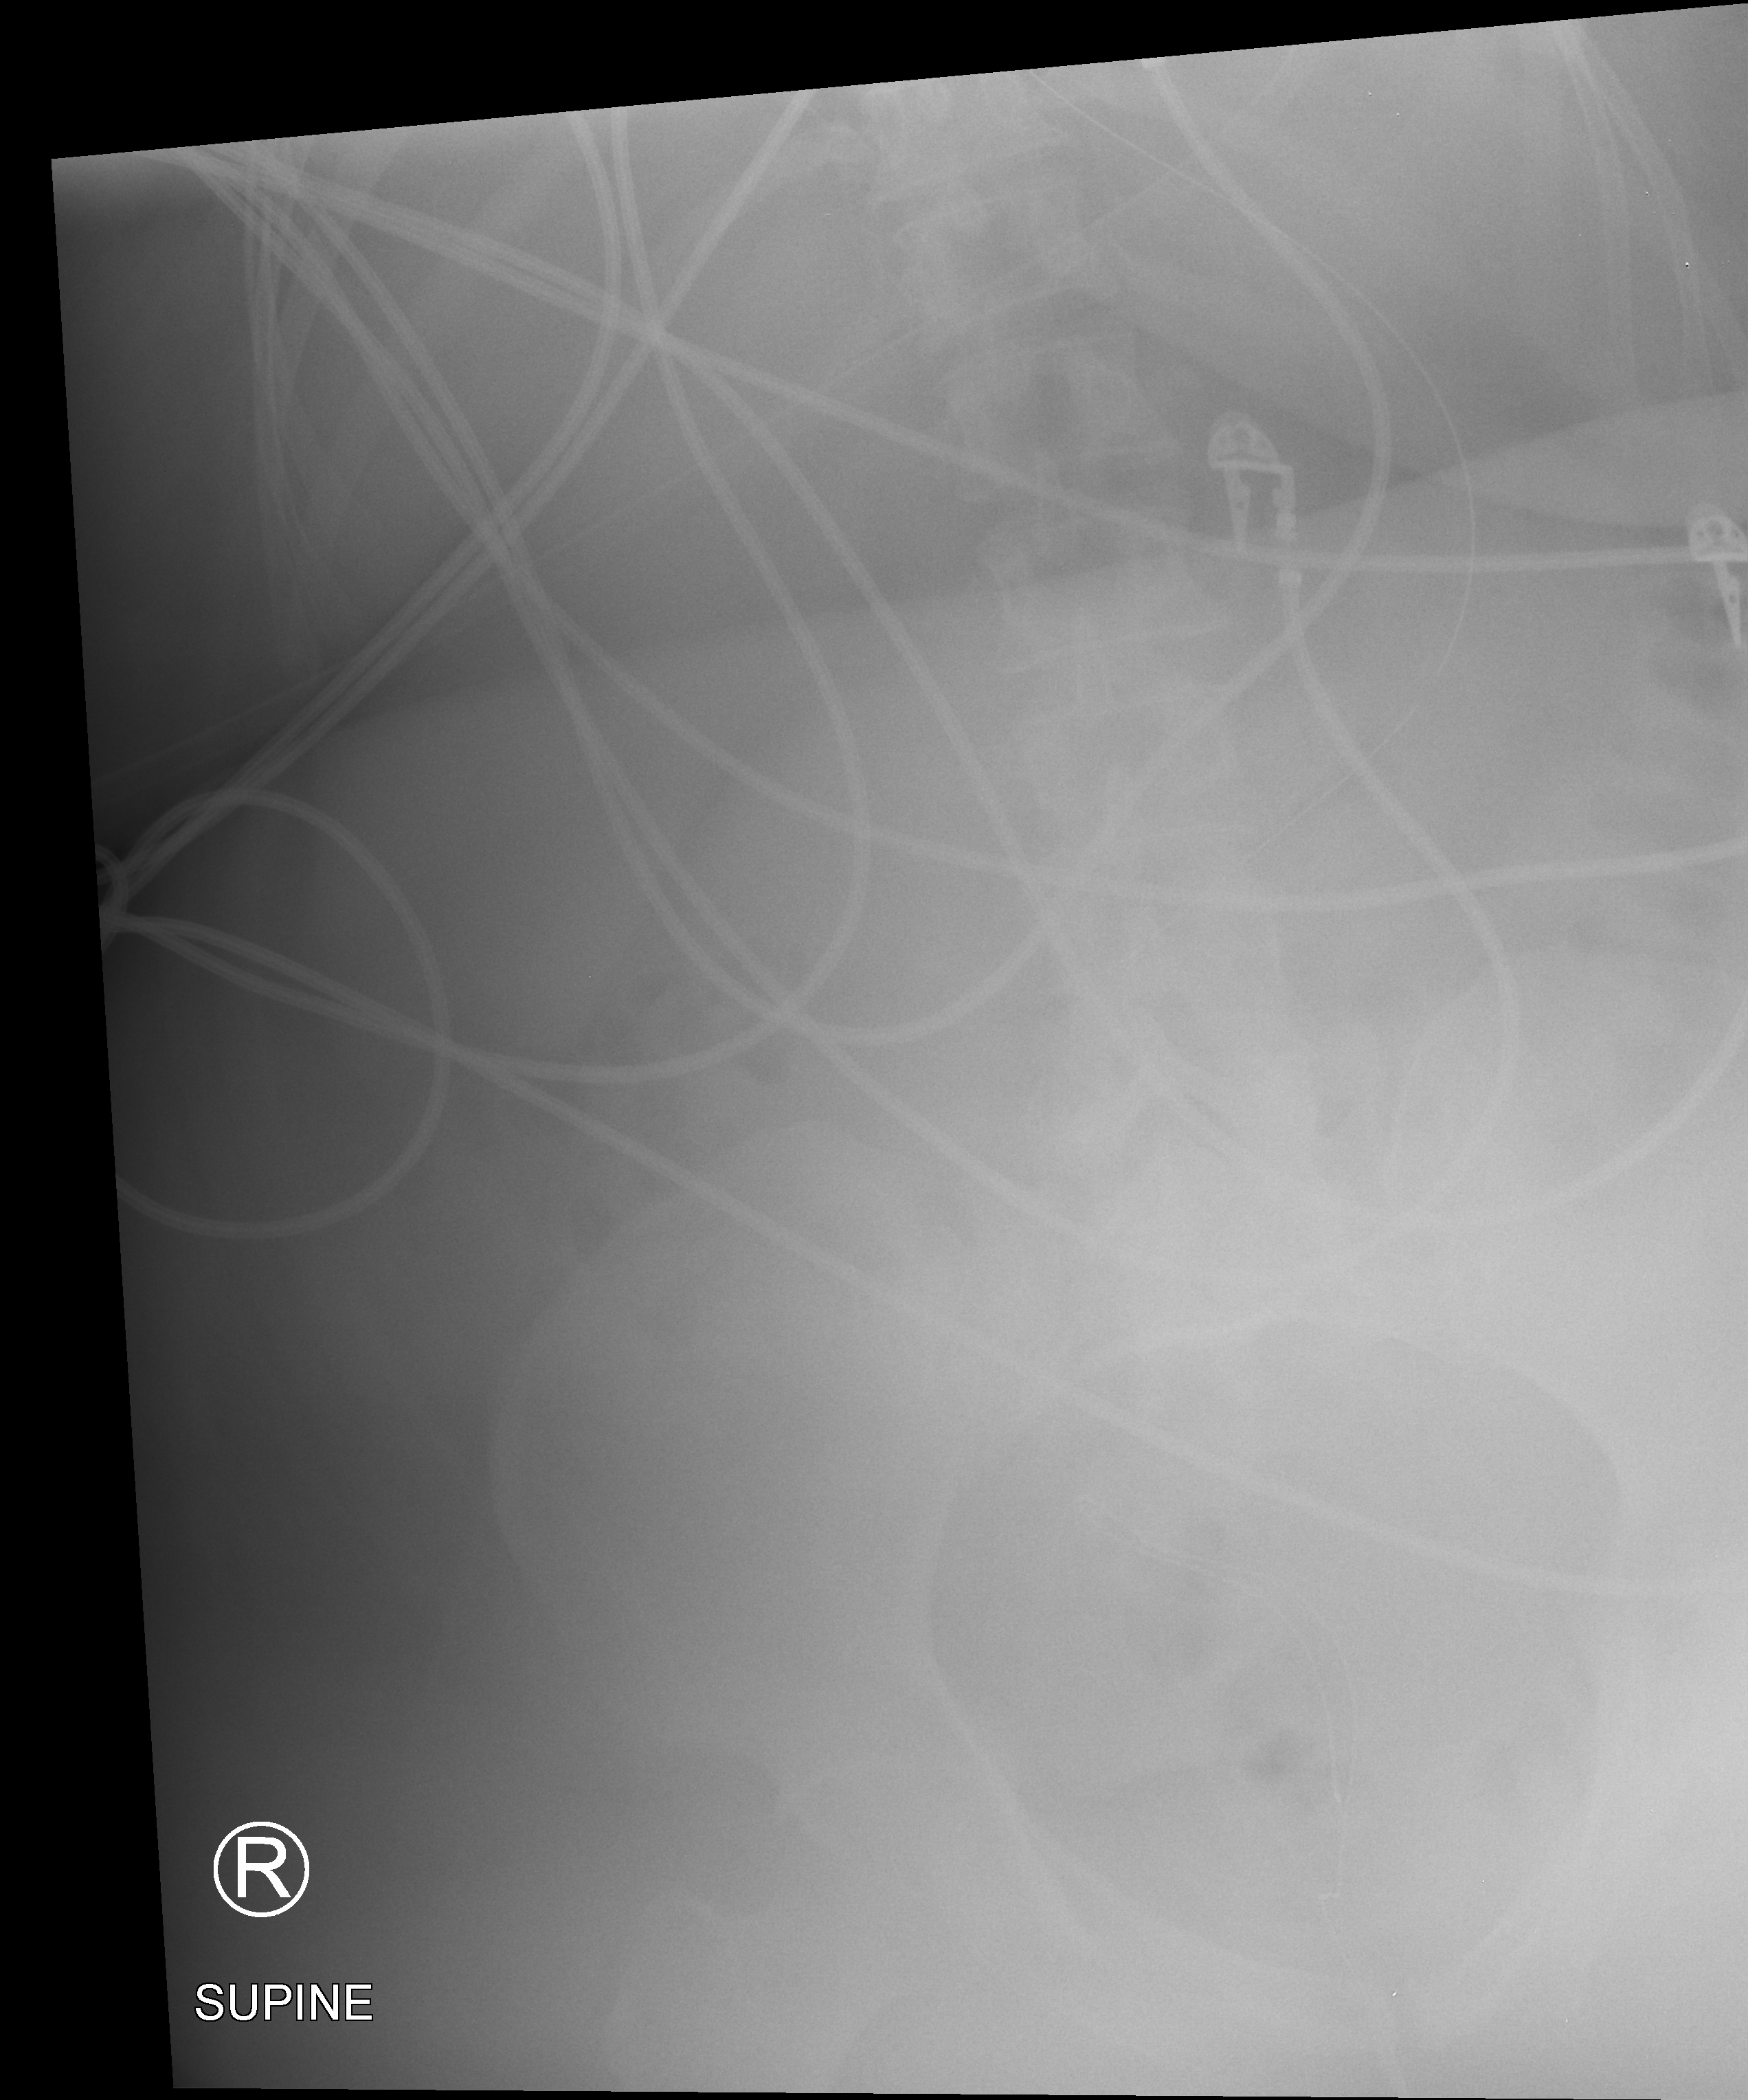
Bedside abdomen radiograph (computed radiography); anteroposterior (AP) projection. Female patient hospitalised with COVID-19, age 18–59 years.
Hospital-stay facts (about this admission, not read from this image; timing relative to this image not recorded):
- mechanically ventilated during this hospital stay: yes
- admitted to intensive care during this hospital stay: yes
- chronic kidney disease (admission record): no